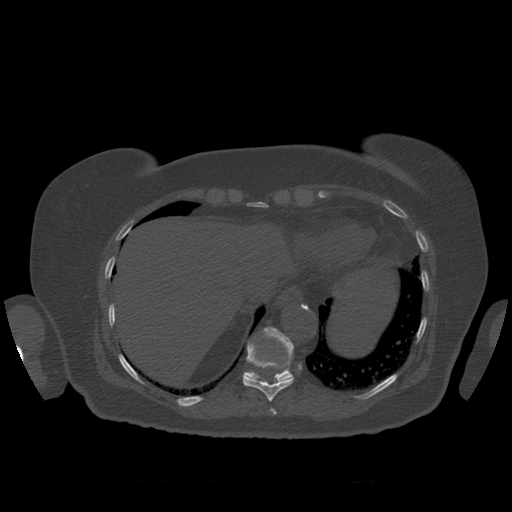
CT including the spine, one axial slice. Slice 335 of 399 in the series (ordered by position). Reconstruction kernel STANDARD. 120 kVp. Bone window (W 1800 / L 400 HU). 512 × 512 image matrix, field of view 404 × 404 mm. Patient age 81 years. From the clinical record (not read from this slice): primary cancer: renal.
Annotated regions visible in this slice (semi-automatic segmentation, software-assisted and operator-edited):
- T10 vertebra: bounding box (x1, y1, x2, y2) in pixels: (243, 344, 294, 402)
- T11 vertebra: (244, 327, 294, 382)
- T9 vertebra: (270, 409, 277, 415)